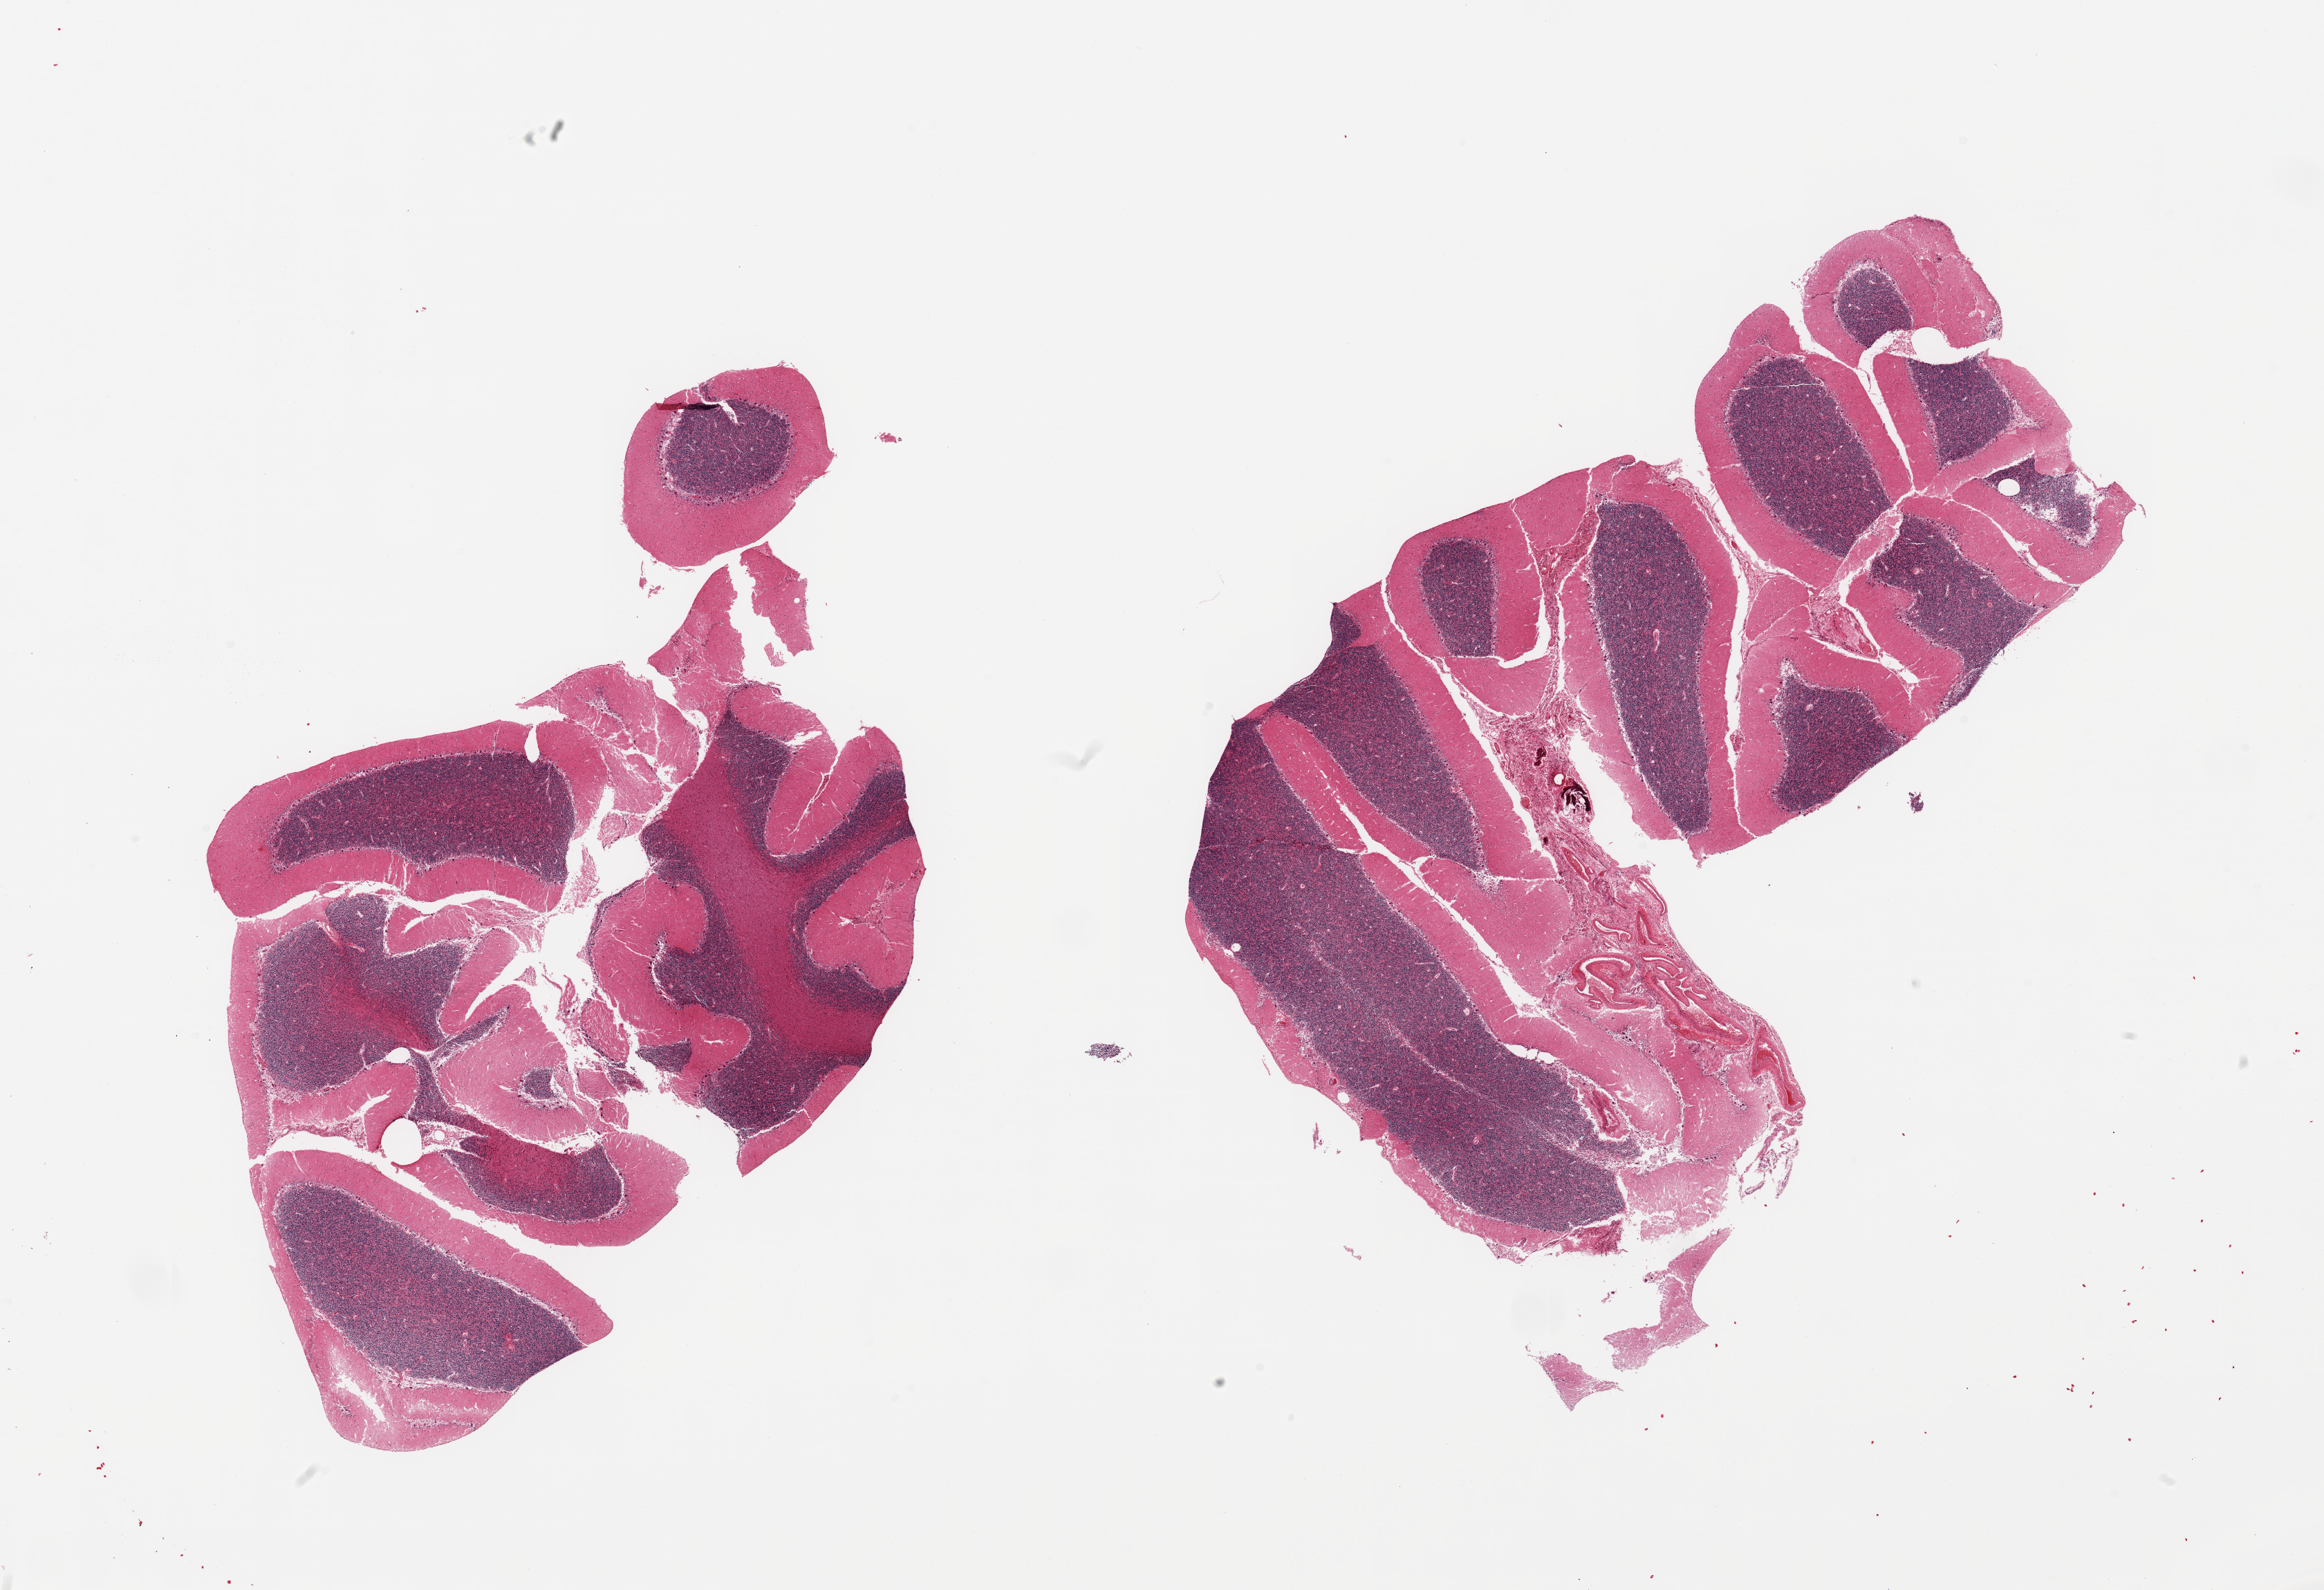
Haematoxylin and eosin whole-slide image, shown as a low-resolution overview of the whole scanned area (about 26.6 x 18.2 mm), PAXgene-fixed paraffin-embedded (PFPE) section, target tissue: cerebellum, tissue donor sample. Male donor.
Review note (as recorded): 2 pieces; Purkinji cells well visualized, focal residual meninges.